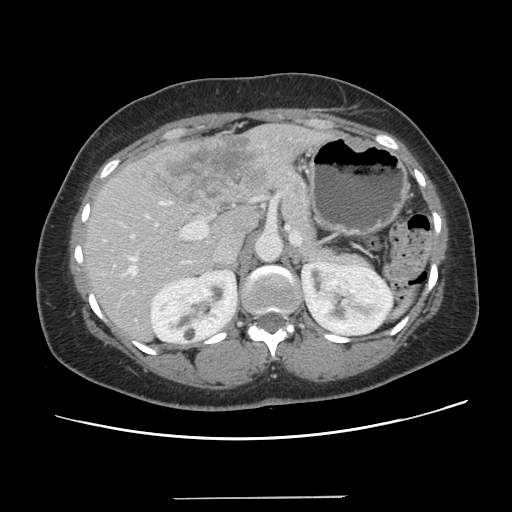
Contrast-enhanced abdominal CT, one axial slice. Position 77 of 141 along the scan axis. 120 kVp. Intravenous contrast given. Soft-tissue window (W 400 / L 40 HU). 512 × 512 image matrix, field of view 366 × 366 mm. Female patient, age 53 years. From the clinical record (not read from this slice): diagnosis: colorectal cancer liver metastases, imaged before liver resection; multiple liver metastases: no; largest metastasis: 14.5 cm.
Structures marked on this image (manually delineated by an expert):
- hepatic veins: bounding box <124,256,136,275> (left, top, right, bottom; pixels)
- liver: <86,124,325,341>
- planned liver remnant (the part of the liver to remain after resection): <86,205,260,341>
- portal vein (with intrahepatic branches): <131,201,208,239>
- liver metastasis: <157,136,264,204>